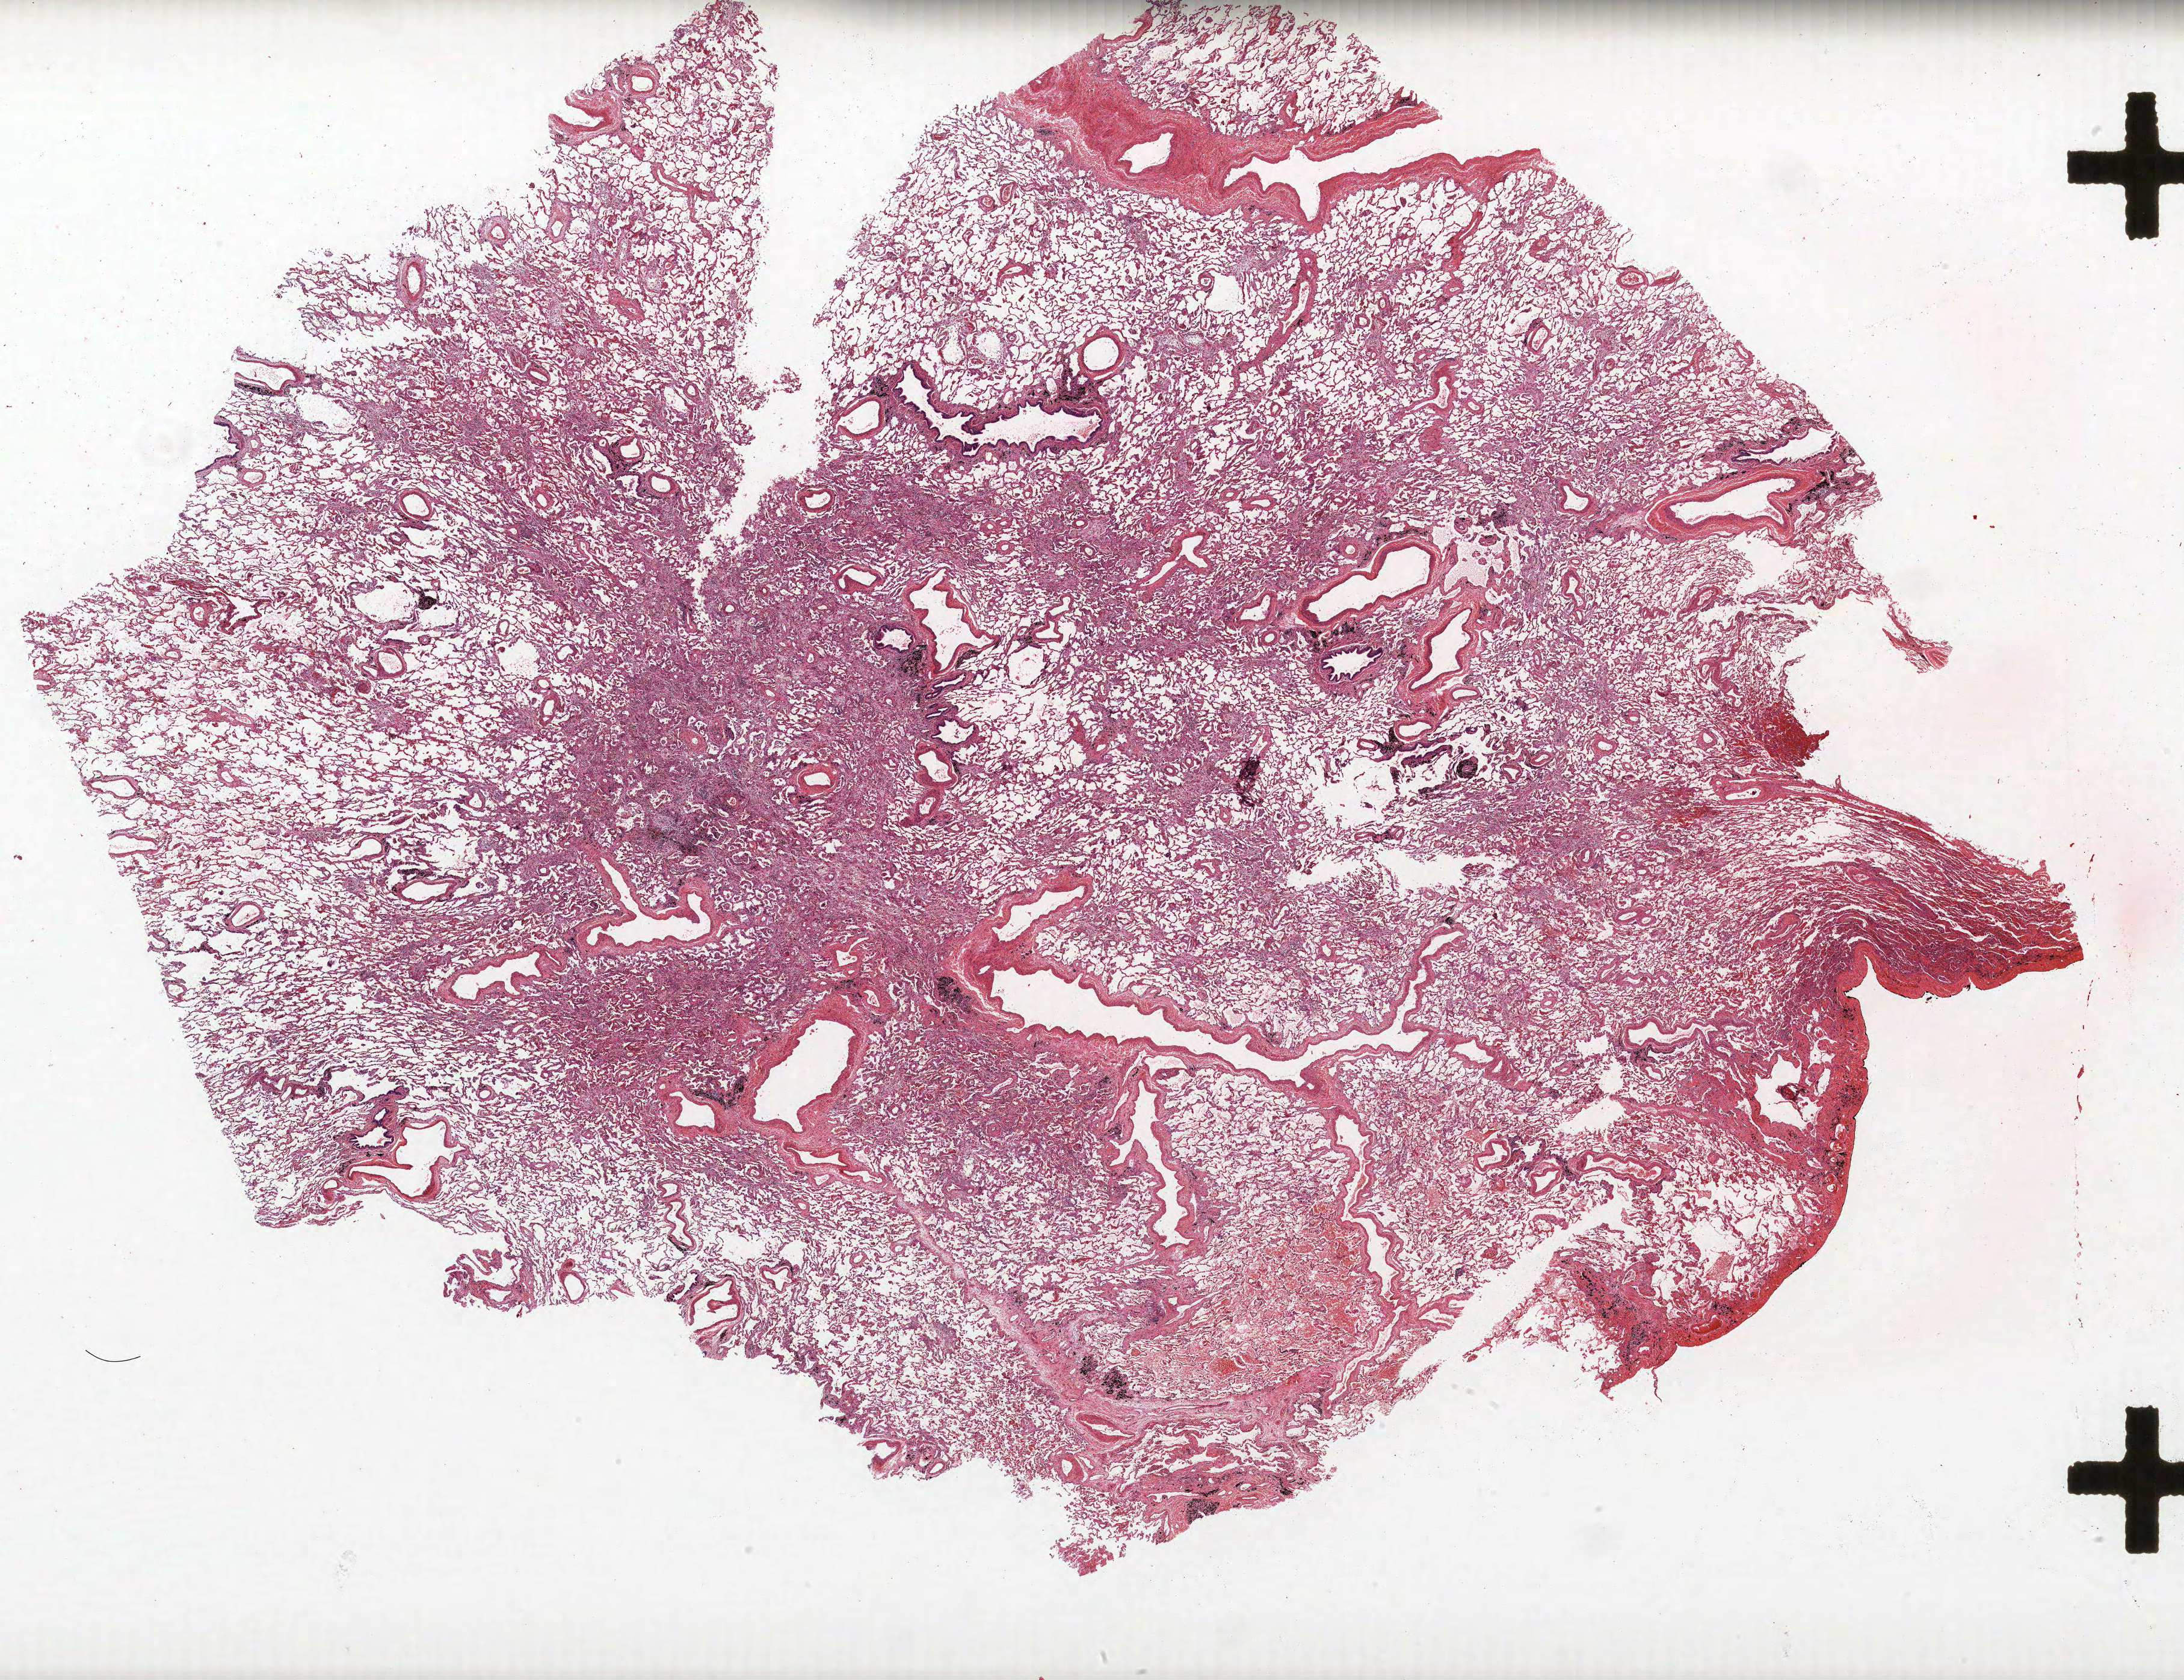
H&E-stained whole-slide image, shown as a low-resolution overview of the whole scanned area (about 29.0 x 22.3 mm, slide scanned at 40x), formalin-fixed paraffin-embedded (FFPE) section, lung. Male patient, aged 60 at enrolment. Former smoker at enrolment.
* primary tumour location (clinical record): right lower lobe
* stage (AJCC 6th edition): IA
* tumour size (pathology): 18 mm
* participant's lung-cancer diagnosis: Adenocarcinoma, NOS